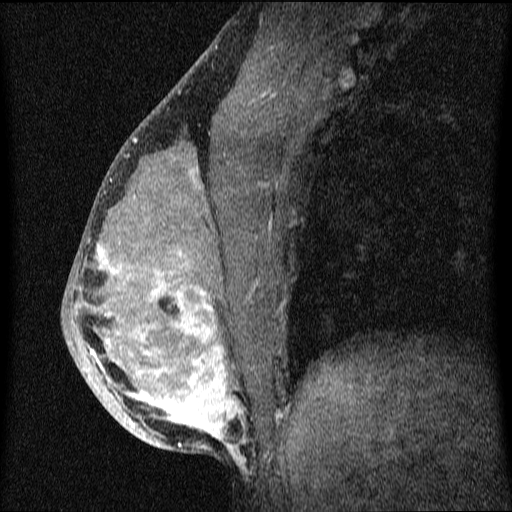
Breast MRI (dynamic contrast-enhanced), one sagittal slice. Slice 32 of 64 in the series (ordered by position). Dynamic contrast-enhanced series, image 2 of 4 at this slice position (ordered by acquisition). 1.5 T. TE 4.2 ms, TR 9.1 ms. 2 mm slice thickness. 512 × 512 image matrix, field of view 180 × 180 mm. Female patient, age 33 years.
Annotated regions visible in this slice (semi-automatically segmented with operator editing):
- analysis volume of interest (the breast-tissue region the enhancement analysis was run in; not a lesion): bounding box [x1, y1, x2, y2] px = [63, 151, 336, 458]
- tumour enhancement mask (voxels above the 70 % enhancement threshold inside the analysis volume of interest): [78, 172, 245, 458]